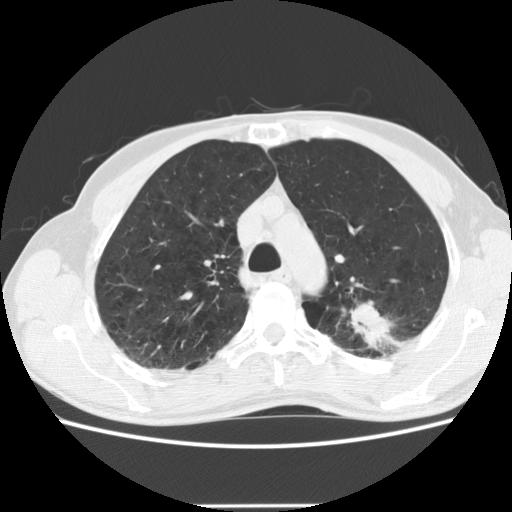
Axial slice from a low-dose chest CT screening exam, first (baseline) screen, lung window (W 1500 / L -600 HU), slice 47 of 191 in the series. Male participant, aged 64 years at enrolment. Current smoker at enrolment.
Lesion marked by an expert reader, bounding box <339,284,435,360> (left, top, right, bottom; pixels). The exam's reader record, not a measurement of the box and not confirmed to be the same lesion: non-calcified nodule or mass ≥4 mm, left upper lobe, 27 × 19 mm, poorly defined margins, soft tissue attenuation. Later outcome: lung cancer diagnosed 23 days after this screen — adenocarcinoma, NOS, left upper lobe, moderately differentiated (G2), stage IA (AJCC 6th edition), 29 mm at pathology.